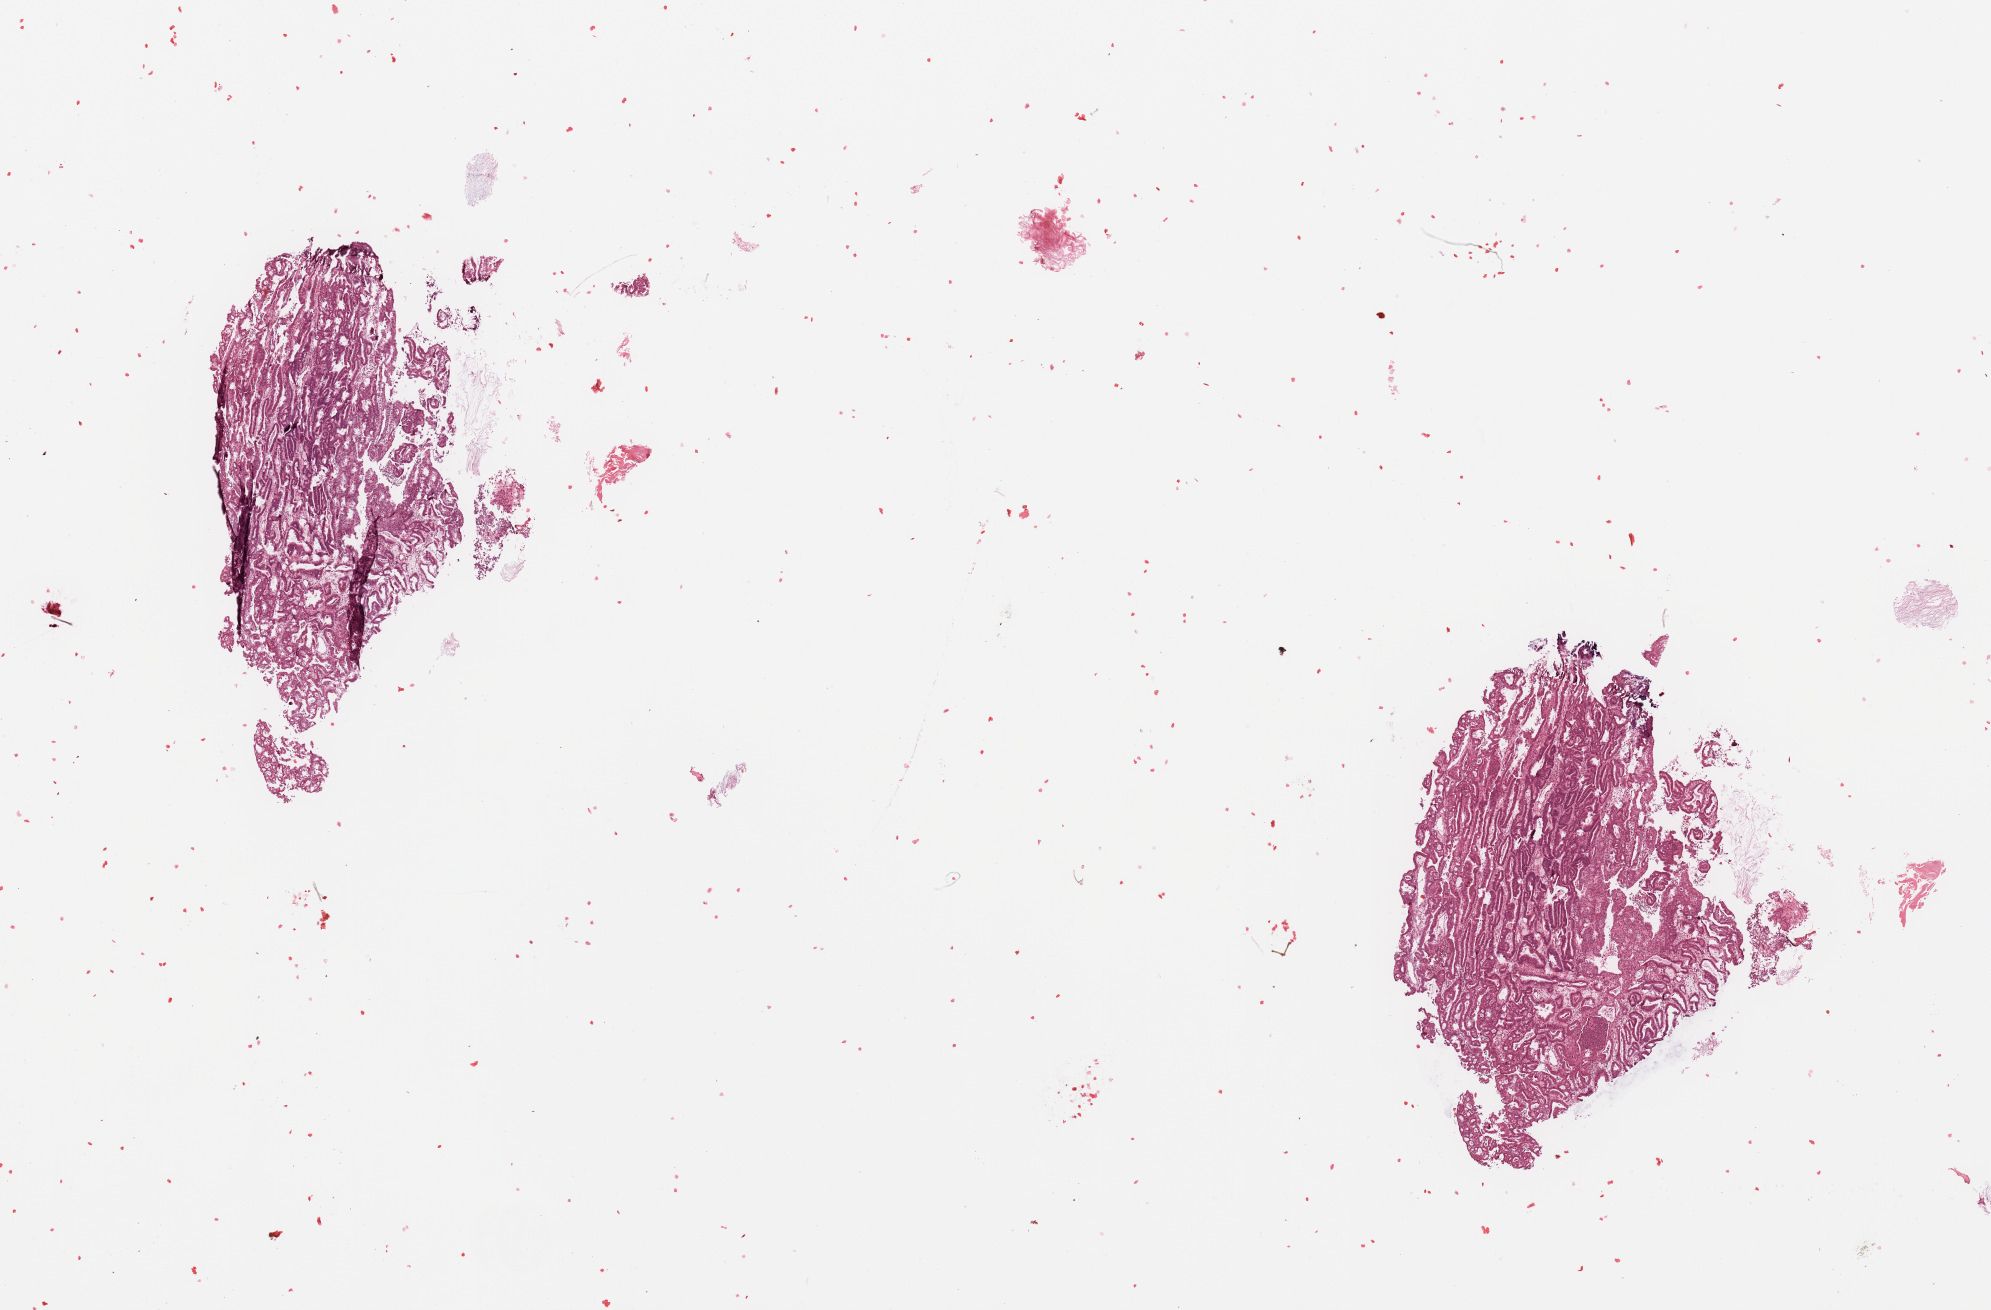
H&E-stained whole-slide image — whole scanned area (about 15.8 x 10.4 mm, slide scanned at 20x) shown as a low-resolution overview; tumour tissue sample, sampled site: uterus. 69-year-old female patient. Histologic grade: G1 (well differentiated). Pathologist review of this section (percent, as recorded): tumour nuclei 90%, necrosis 2%.
* primary tumour site (as recorded): anterior endometrium
* AJCC pathologic stage: I
* histologic diagnosis: Endometrioid adenocarcinoma, NOS